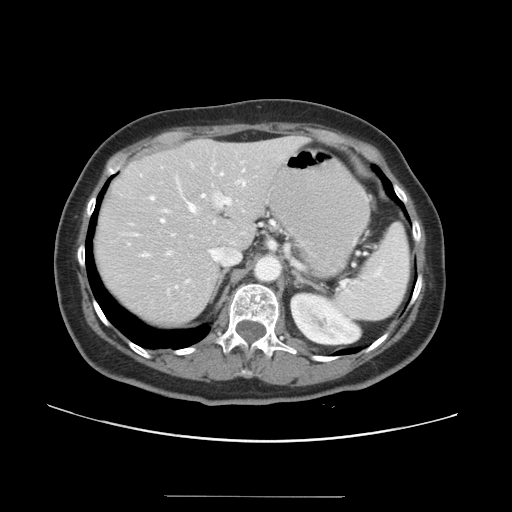
Contrast-enhanced abdominal CT, one axial slice. Position 24 of 34 along the scan axis. Reconstruction kernel STANDARD. 120 kVp. Intravenous contrast given. Soft-tissue window (W 400 / L 40 HU). 5 mm slice thickness. 512 × 512 image matrix, field of view 382 × 382 mm. Female patient, age 69 years. Case-level facts recorded for this patient, not image findings: diagnosis: colorectal cancer liver metastases, imaged before liver resection; multiple liver metastases: yes; largest metastasis: 1.4 cm; disease in both lobes: yes.
Outlined on this slice (outlined manually by an expert reader):
- hepatic veins: bounding box <164,165,245,287> (left, top, right, bottom; pixels)
- liver: <94,137,307,326>
- planned liver remnant (the part of the liver to remain after resection): <94,137,307,326>
- portal vein (with intrahepatic branches): <141,174,346,286>